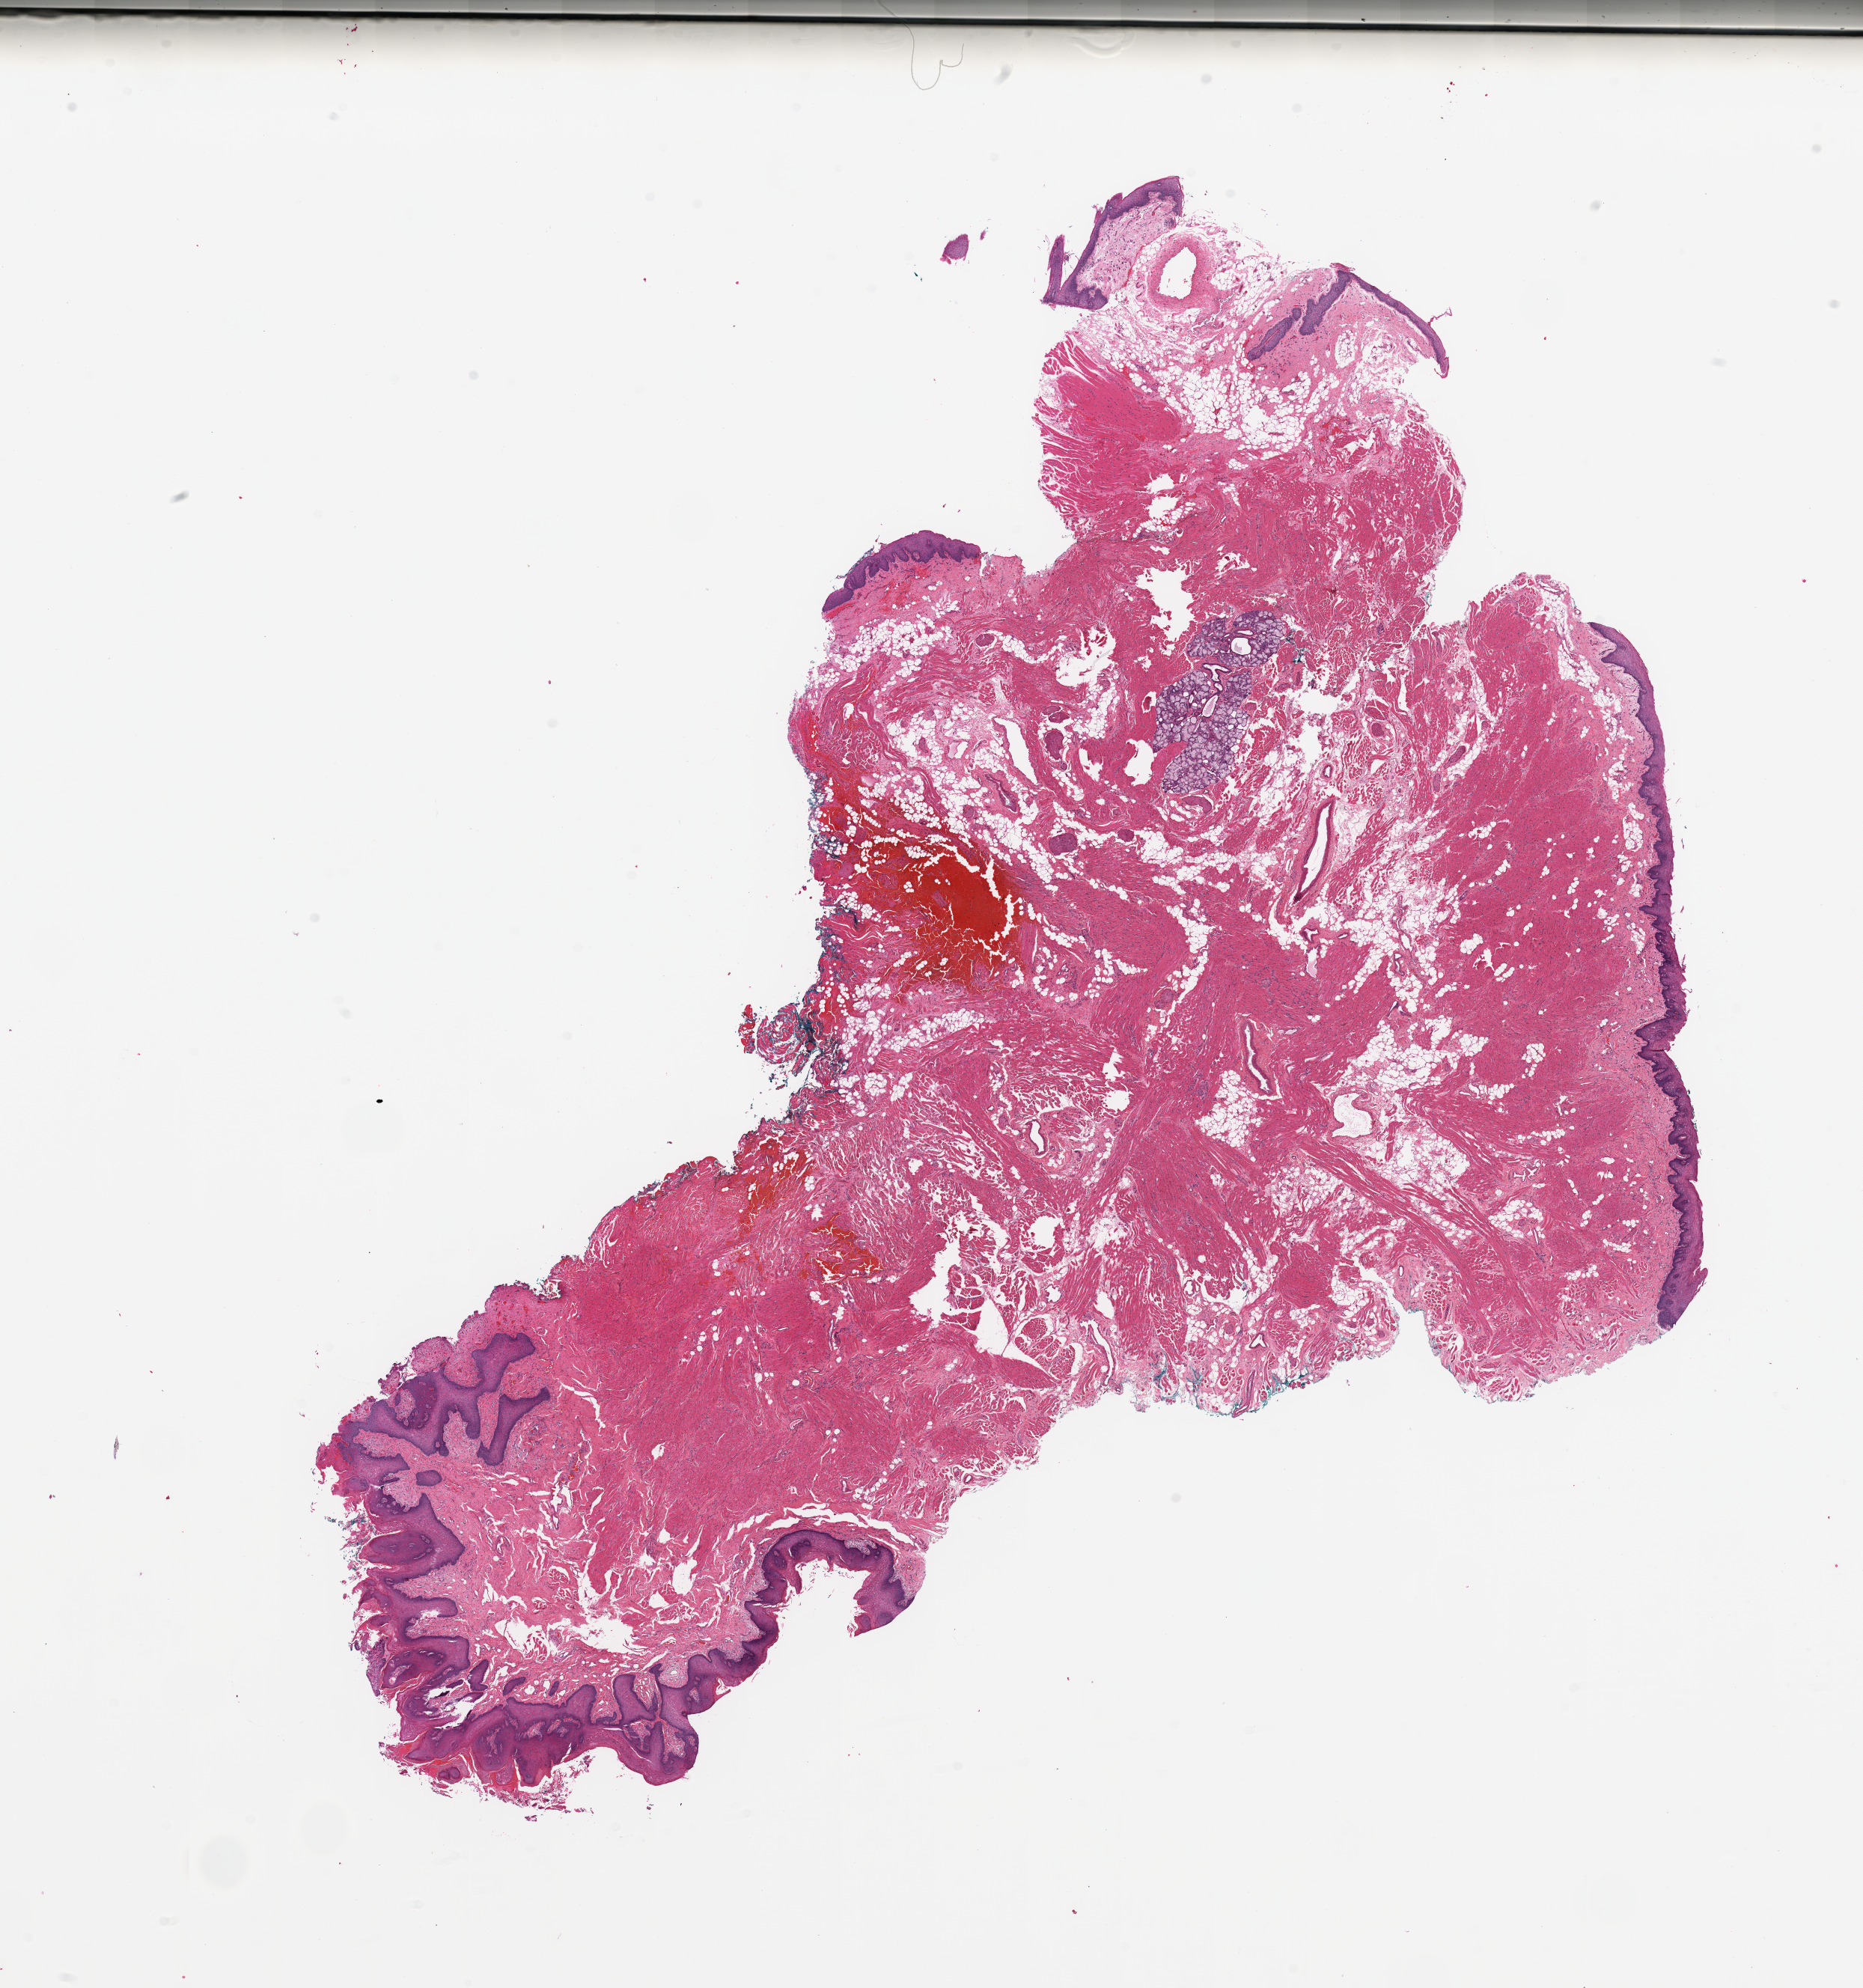
Whole-slide histology image, Hematoxylin and eosin (H&E) stained, low-resolution overview of the scanned area, about 19.7 x 21.0 mm, normal (non-tumour) tissue sample, sampled site: tongue. 50-year-old male patient.
This section: normal (non-tumour) tissue from the same patient. Patient diagnosis: Squamous cell carcinoma, NOS (tongue, NOS).